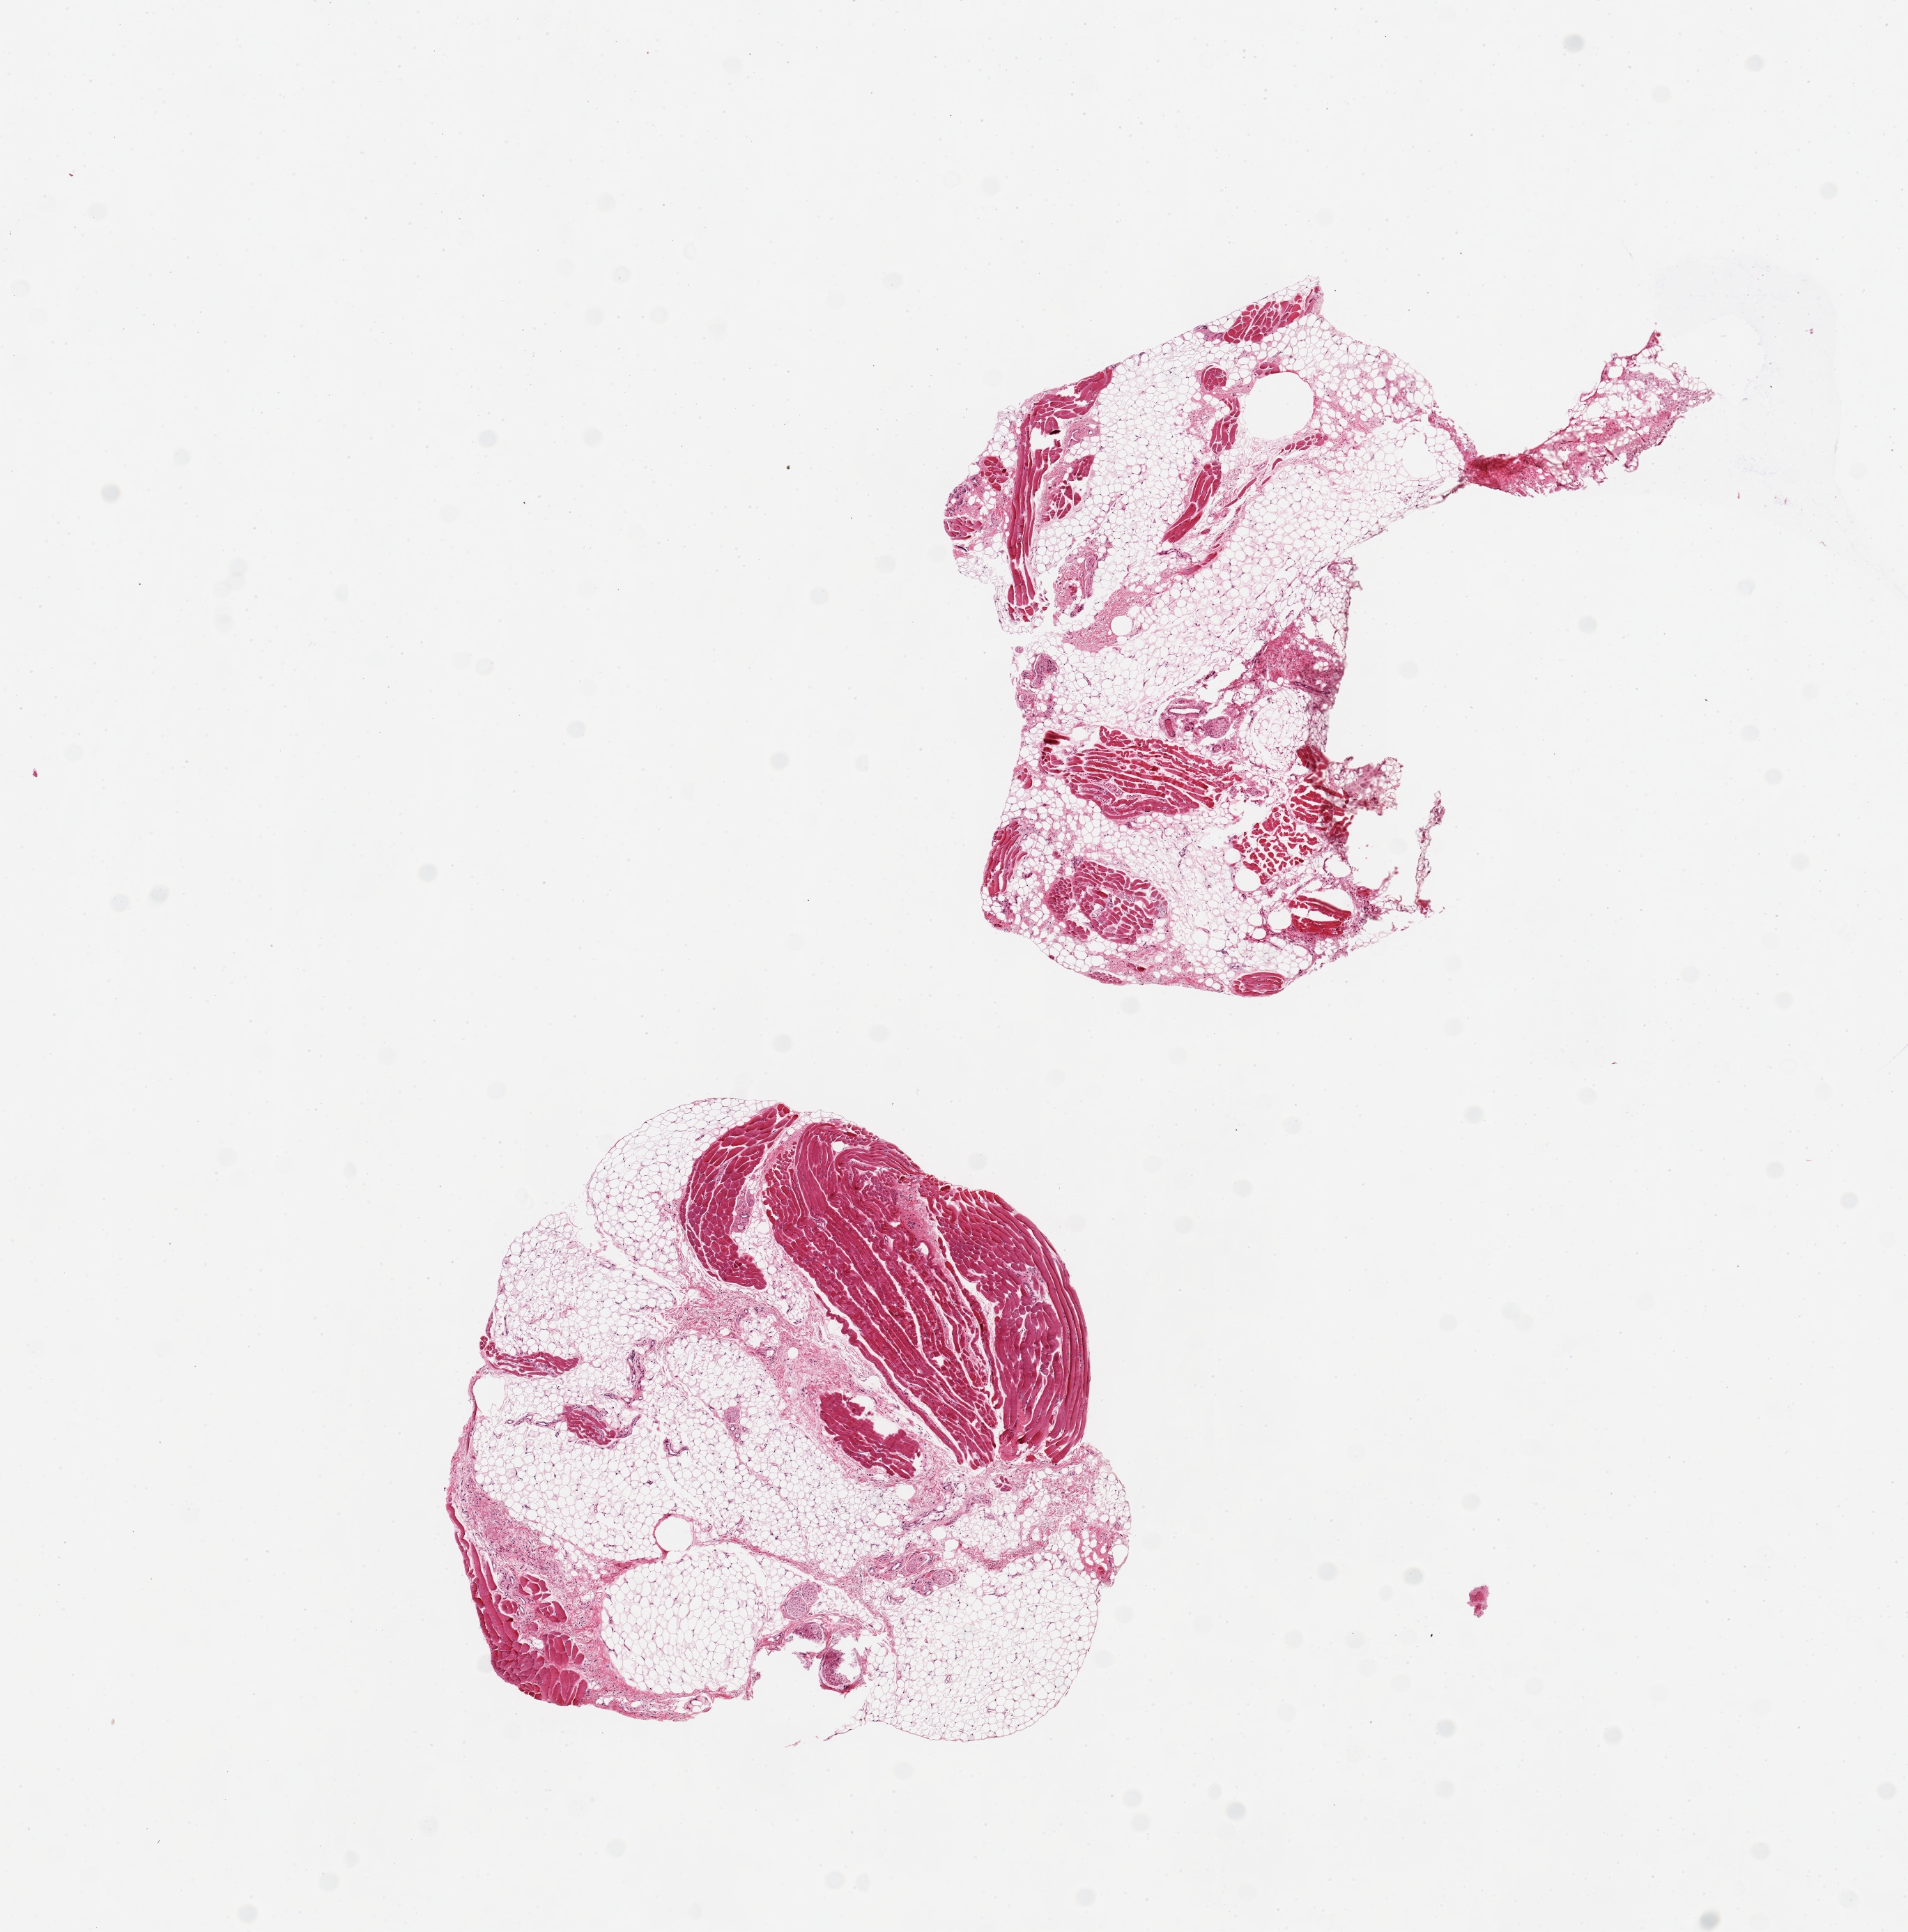
Whole-slide image, hematoxylin and eosin (H&E) stain — shown as a low-resolution overview of the whole scanned area (about 10.8 x 11.0 mm); PAXgene-fixed, paraffin-embedded tissue; section of minor salivary gland (target tissue); tissue donor sample. Female donor.
Review note (as recorded): 2 pieces, 4x4 & 4x4mm; all fat/skeletal muscle, no glandular elements.